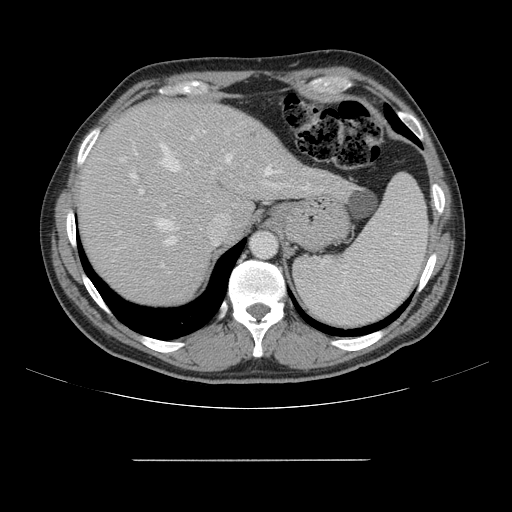
Contrast-enhanced abdominal CT, one axial slice; slice 118 of 164 in the series (ordered by position); intravenous contrast given; soft-tissue window (W 400 / L 40 HU); 2.5 mm slice thickness; 512 × 512 image matrix, field of view 404 × 404 mm. Male patient, age 54 years. Case-level facts recorded for this patient, not image findings: diagnosis: colorectal cancer liver metastases, imaged before liver resection; multiple liver metastases: yes; largest metastasis: 1 cm; disease in both lobes: no.
Structures marked on this image (expert manual segmentation):
- hepatic veins: bounding box (x1, y1, x2, y2) in pixels: (157, 144, 281, 245)
- liver: (79, 103, 346, 303)
- planned liver remnant (the part of the liver to remain after resection): (79, 103, 250, 303)
- portal vein (with intrahepatic branches): (120, 125, 308, 274)